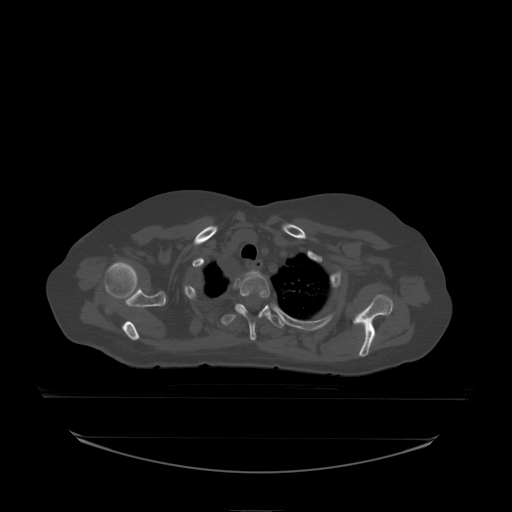
CT including the spine, one axial slice; slice 178 of 242 in the series (ordered by position); bone window (W 1800 / L 400 HU); 2.5 mm slice thickness; 512 × 512 image matrix, field of view 500 × 500 mm. Patient: female, 53 years. From the clinical record (not read from this slice): primary cancer: lung.
Structures marked on this image (semi-automatically segmented with operator editing):
- T1 vertebra: bounding box (x1, y1, x2, y2) in pixels: (241, 270, 261, 278)
- T2 vertebra: (235, 276, 270, 338)
- T3 vertebra: (222, 304, 285, 329)